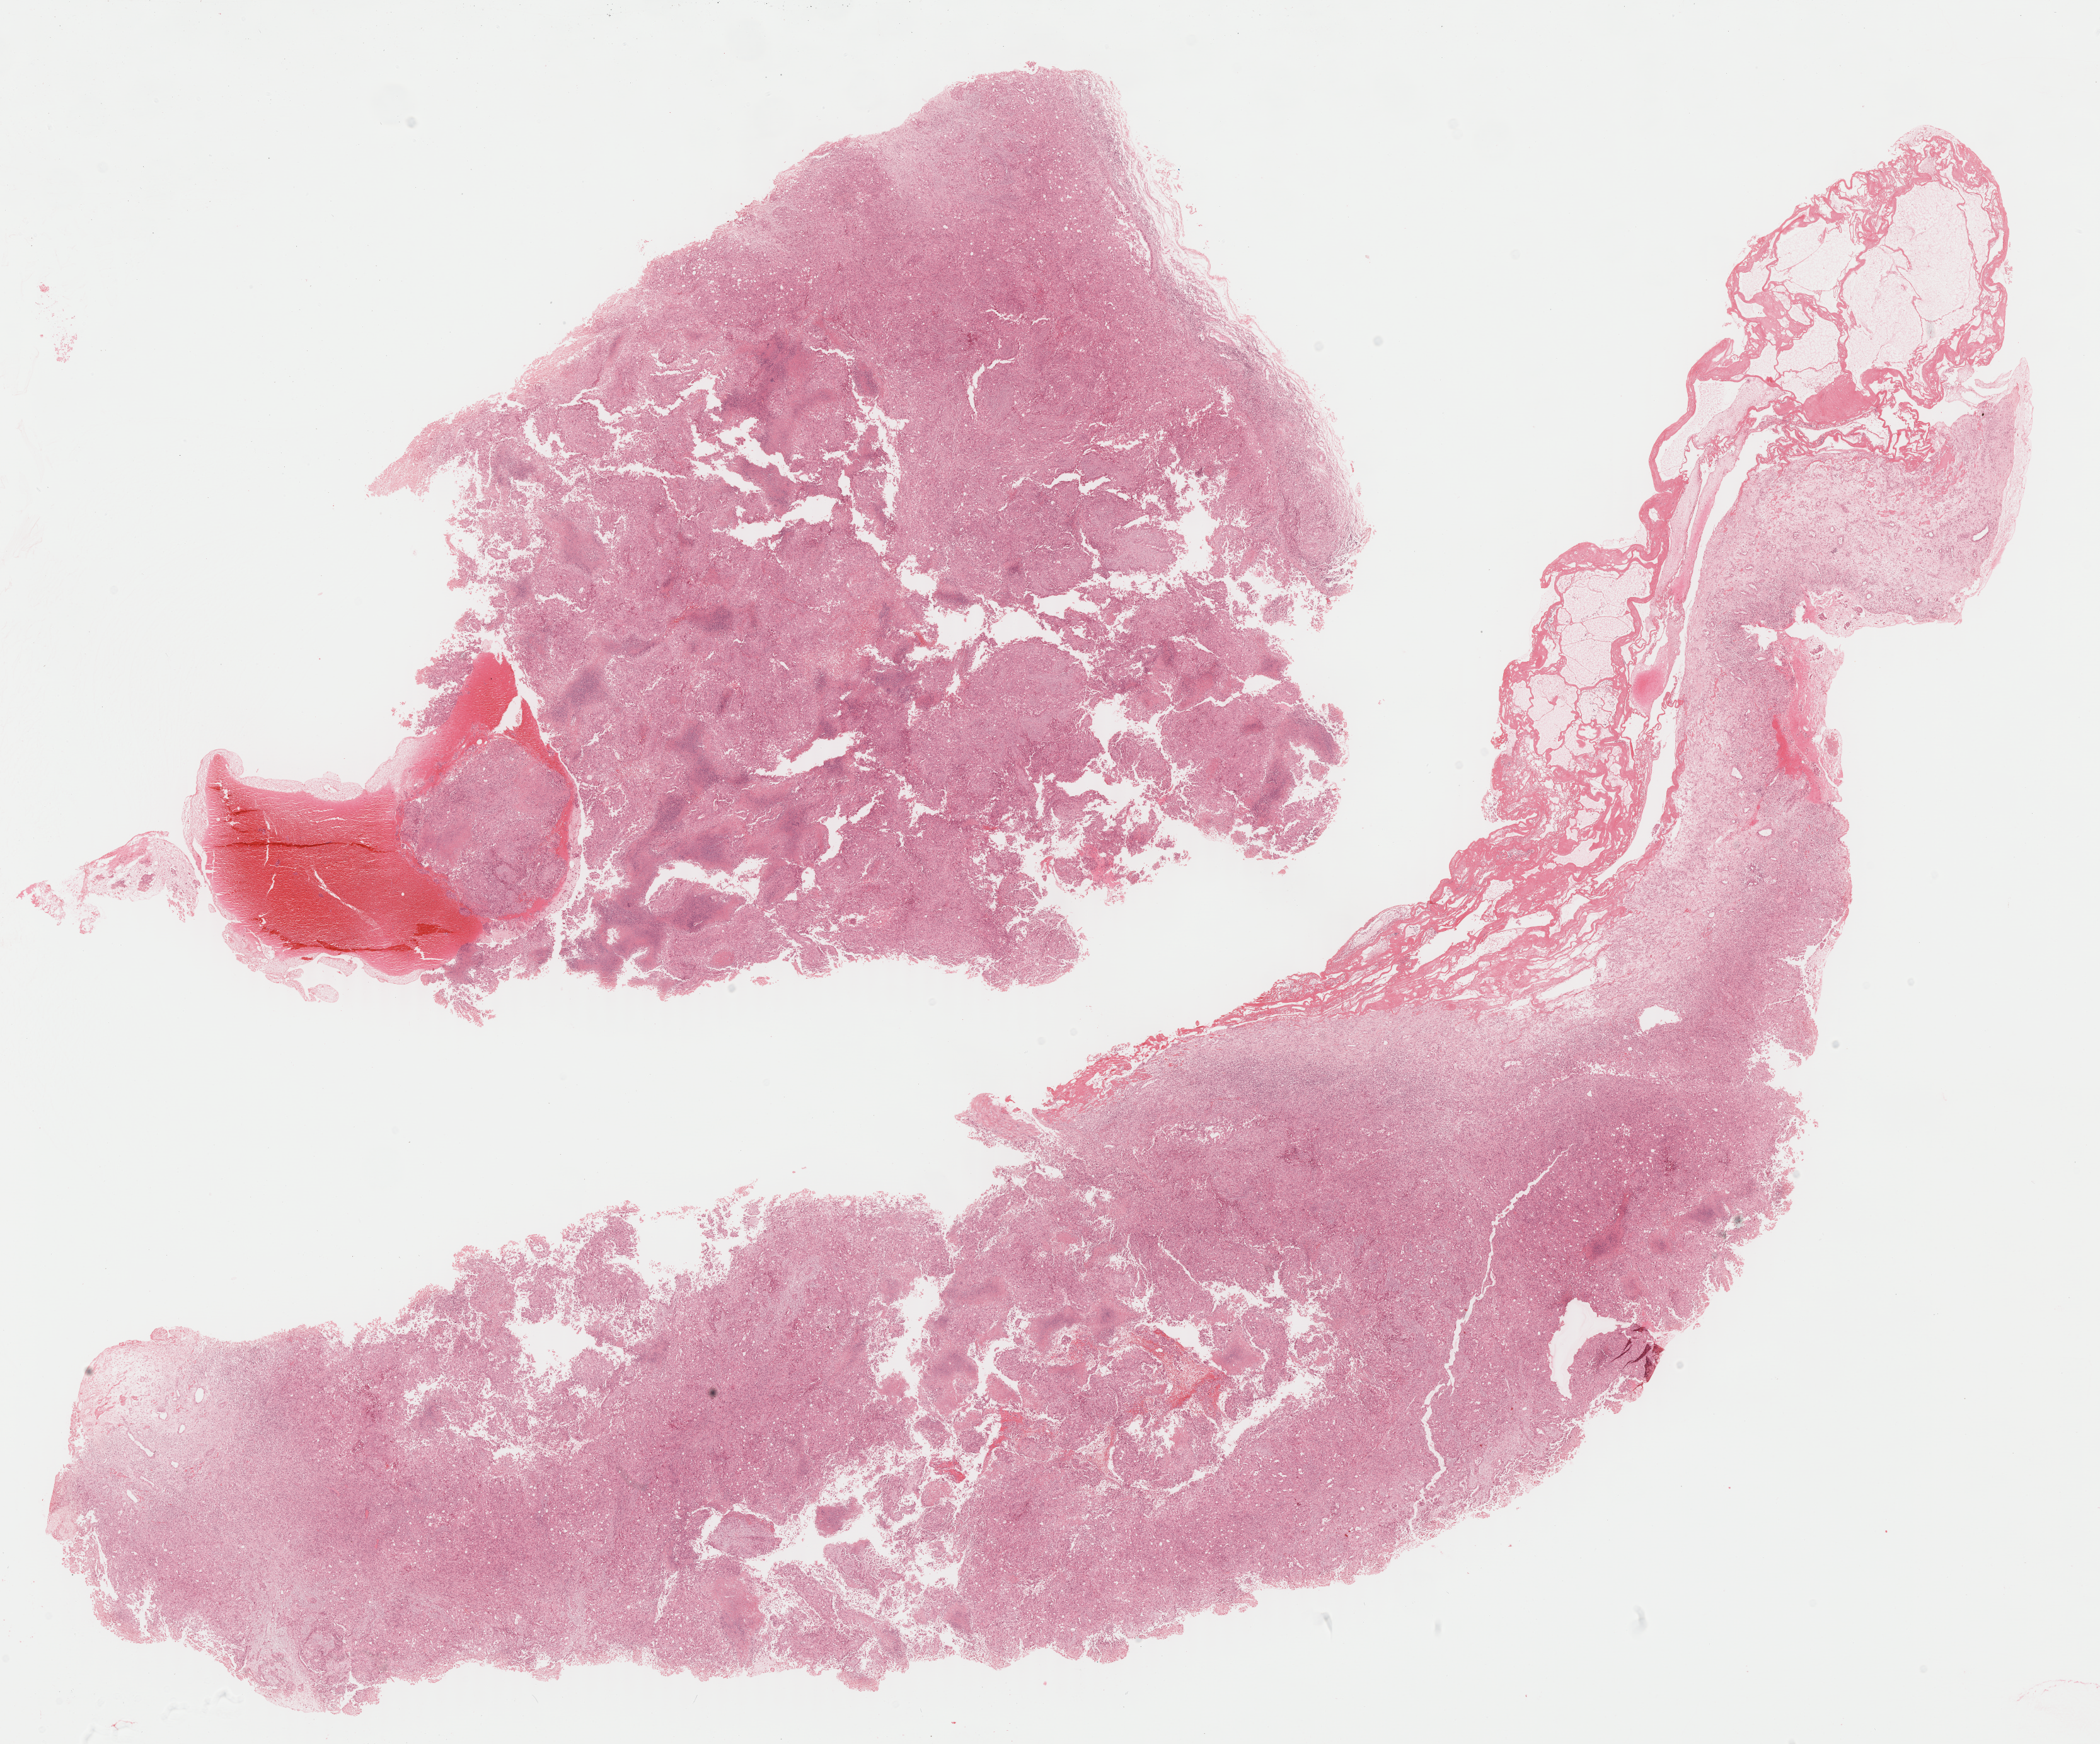
Digitized H&E tissue section (whole slide), a low-resolution overview of the entire scanned area, about 26.3 x 21.9 mm (from a 40x scan). Formalin-fixed paraffin-embedded (FFPE) diagnostic section. Mesothelium, primary tumour sample. Female, age 71 years at initial diagnosis.
TNM: T2 N2 M0. AJCC pathologic stage: III (6th edition). Pathologic diagnosis: Epithelioid mesothelioma, malignant (pleura, NOS).